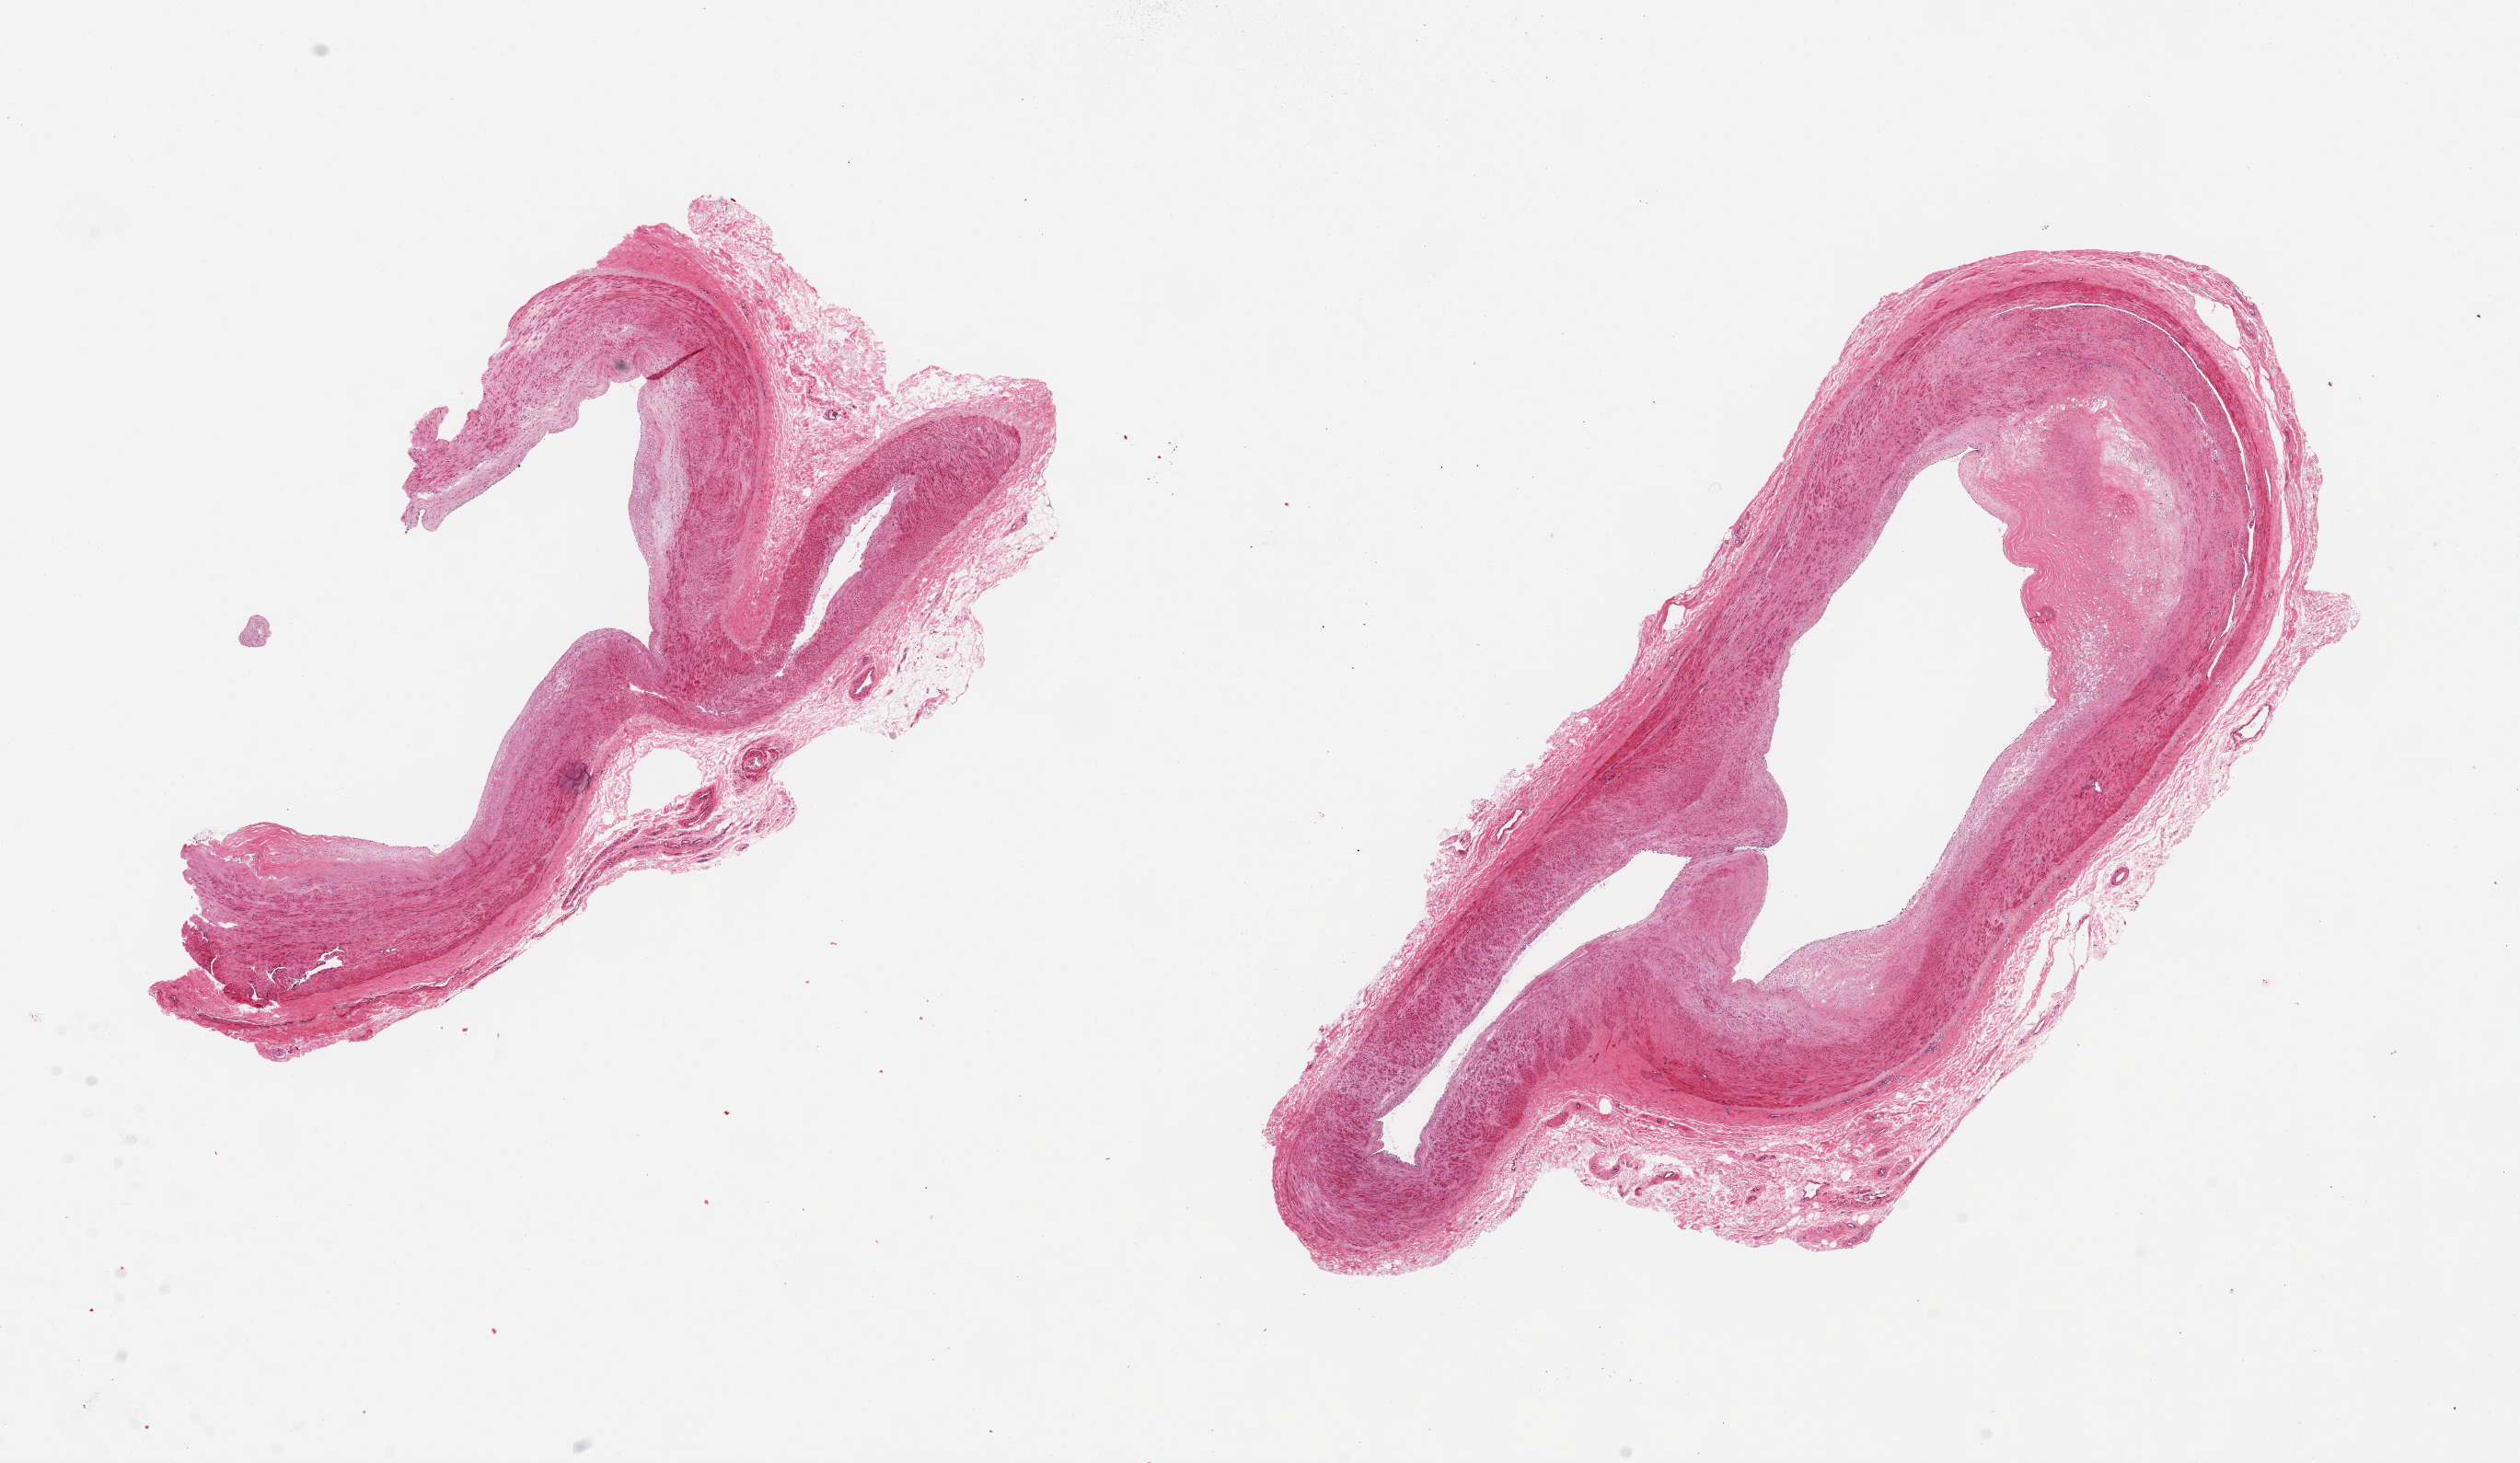
Hematoxylin and eosin (H&E) whole-slide image, brightfield, whole scanned area (about 21.7 x 12.6 mm) shown as a low-resolution overview; PAXgene-fixed paraffin-embedded (PFPE) section; section of tibial artery (target tissue); donor tissue sample. Male donor.
Review note (as recorded): 2 pieces ~8x6mm. 20% occlusive atherosclerosis, relatively clean specimens.